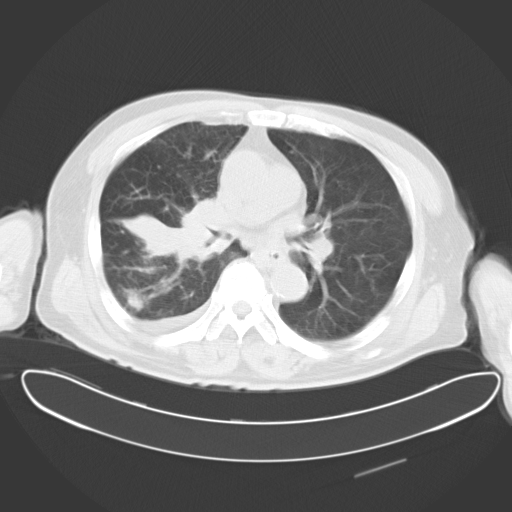
Chest CT, one axial slice. Slice 16 of 30 in the series (ordered by position). Reconstruction kernel B40f. Lung window (W 1500 / L -600 HU). 10 mm slice thickness. 512 × 512 image matrix. Patient: male, 78 years. Case-level facts recorded for this patient, not image findings: clinical TNM (as recorded): T2 N1 M1.
Annotated regions visible in this slice (rectangle marked by the reading radiologist):
- lung tumour (recorded histology: adenocarcinoma): bounding box [x1, y1, x2, y2] px = [113, 174, 228, 271]